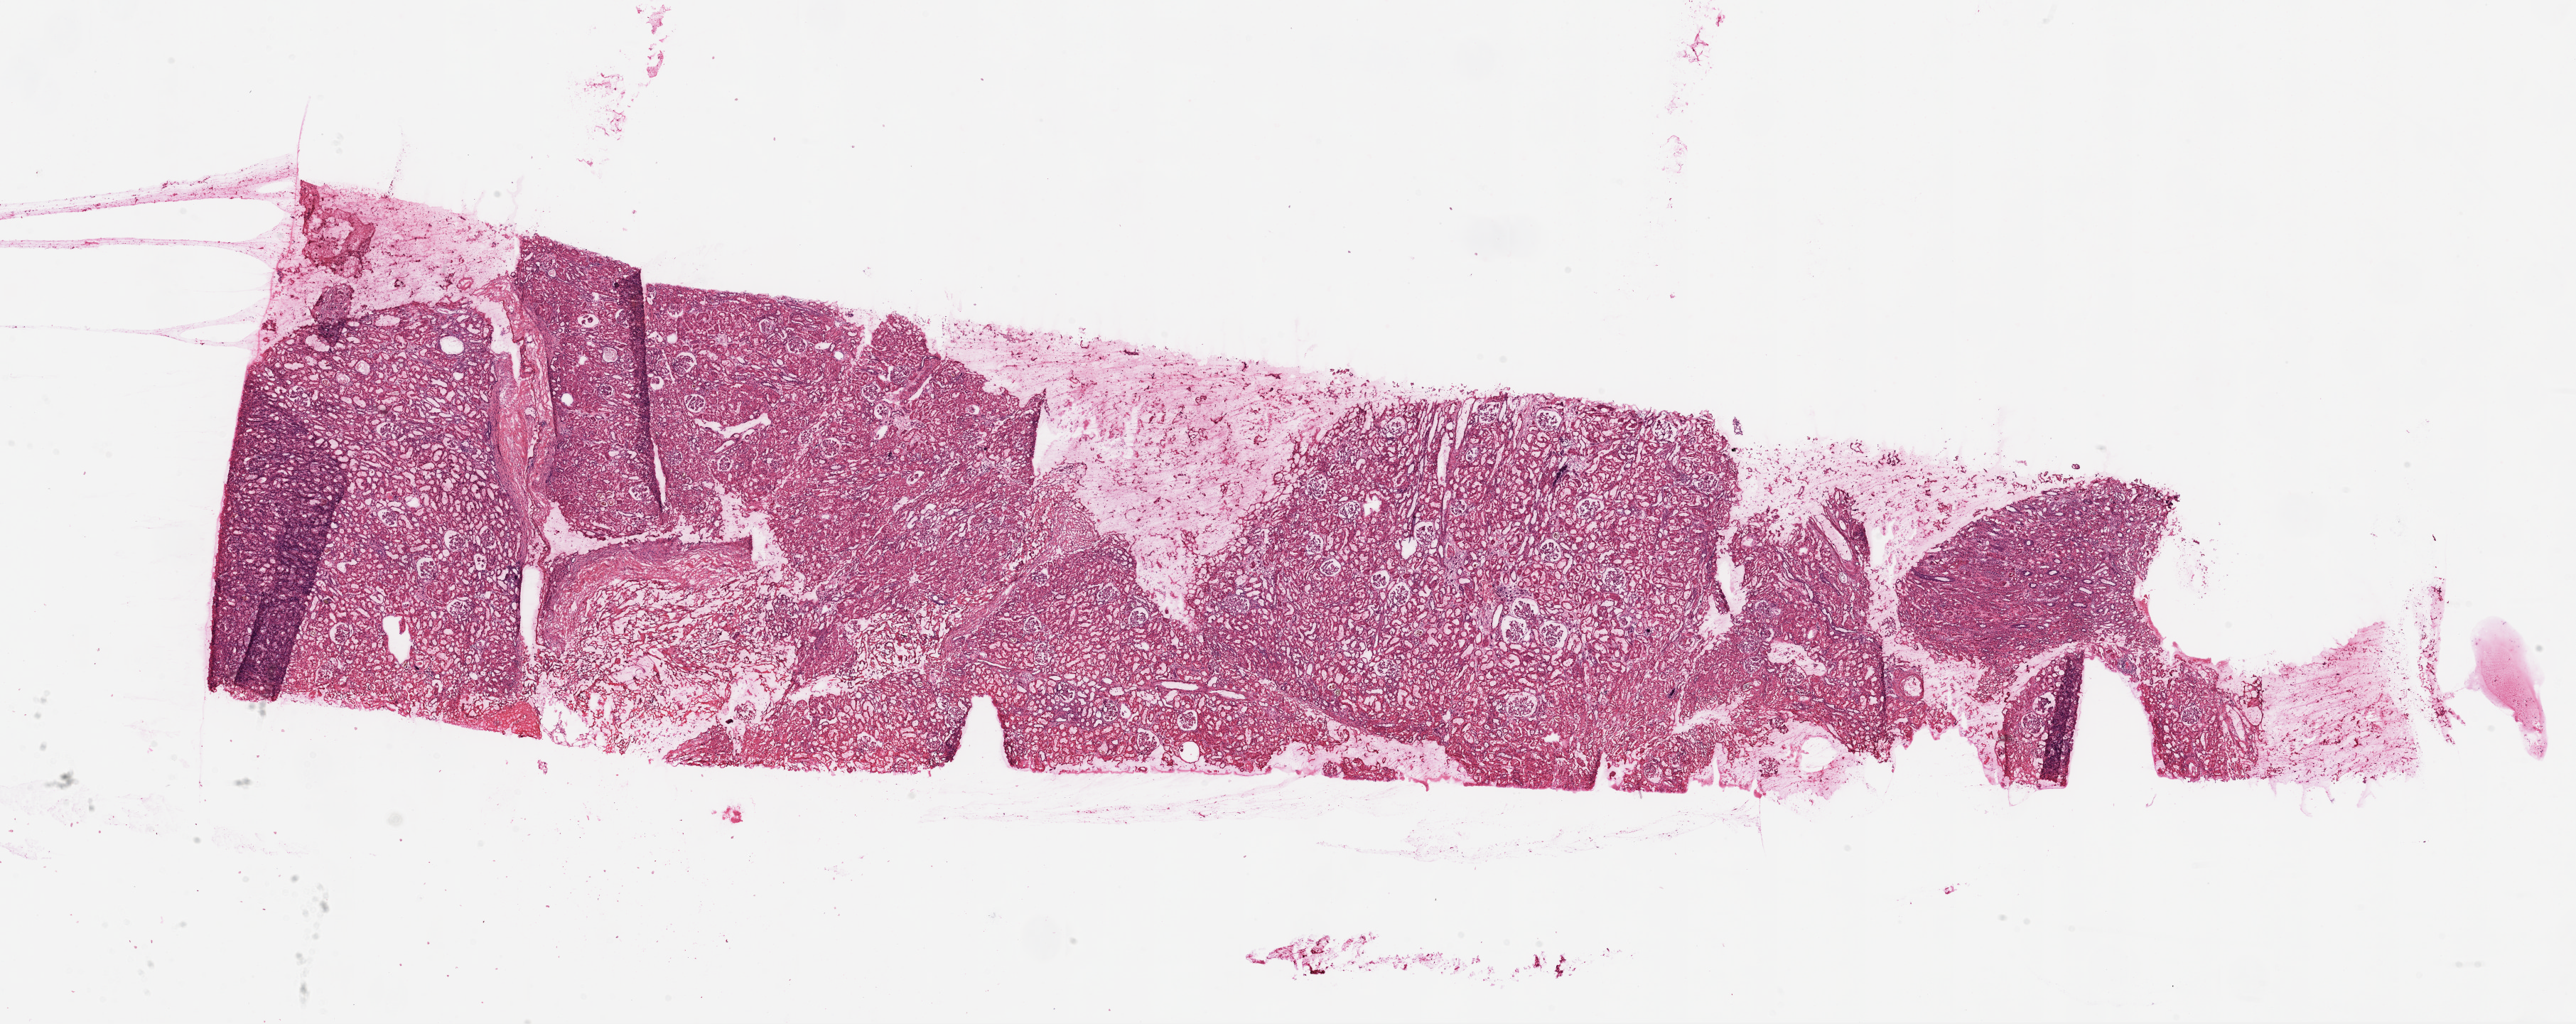
Whole-slide histology image, Hematoxylin and eosin (H&E) stained — low-resolution overview of the scanned area, about 29.1 x 11.6 mm (slide scanned at 20x), frozen section, sample: solid tissue normal (non-tumour tissue), kidney. Male, age 59 years at initial diagnosis.
- this section: solid tissue normal sample (biorepository sample class)
- patient diagnosis: Clear cell adenocarcinoma, NOS